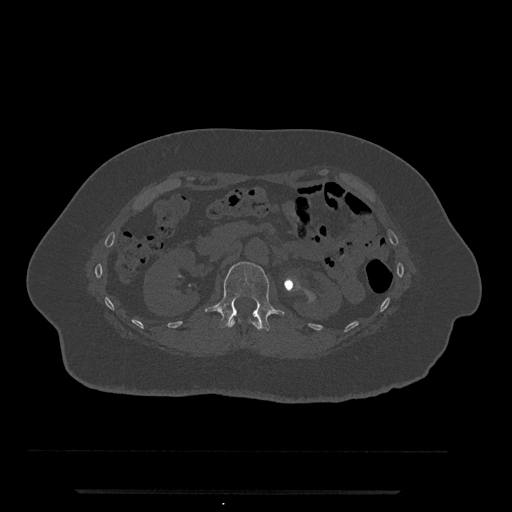
CT including the spine, one axial slice. Position 117 of 797 along the scan axis. 120 kVp. Bone window (W 1800 / L 400 HU). 0.5 mm slice thickness. 512 × 512 image matrix, field of view 440 × 440 mm. Female patient, age 51 years. Case-level facts recorded for this patient, not image findings: primary cancer: neuro; vertebrae with lytic lesions (as recorded): T8.
Outlined on this slice (semi-automatically segmented with operator editing):
- L1 vertebra: bounding box <205,262,285,331> (left, top, right, bottom; pixels)
- T12 vertebra: <229,318,262,330>